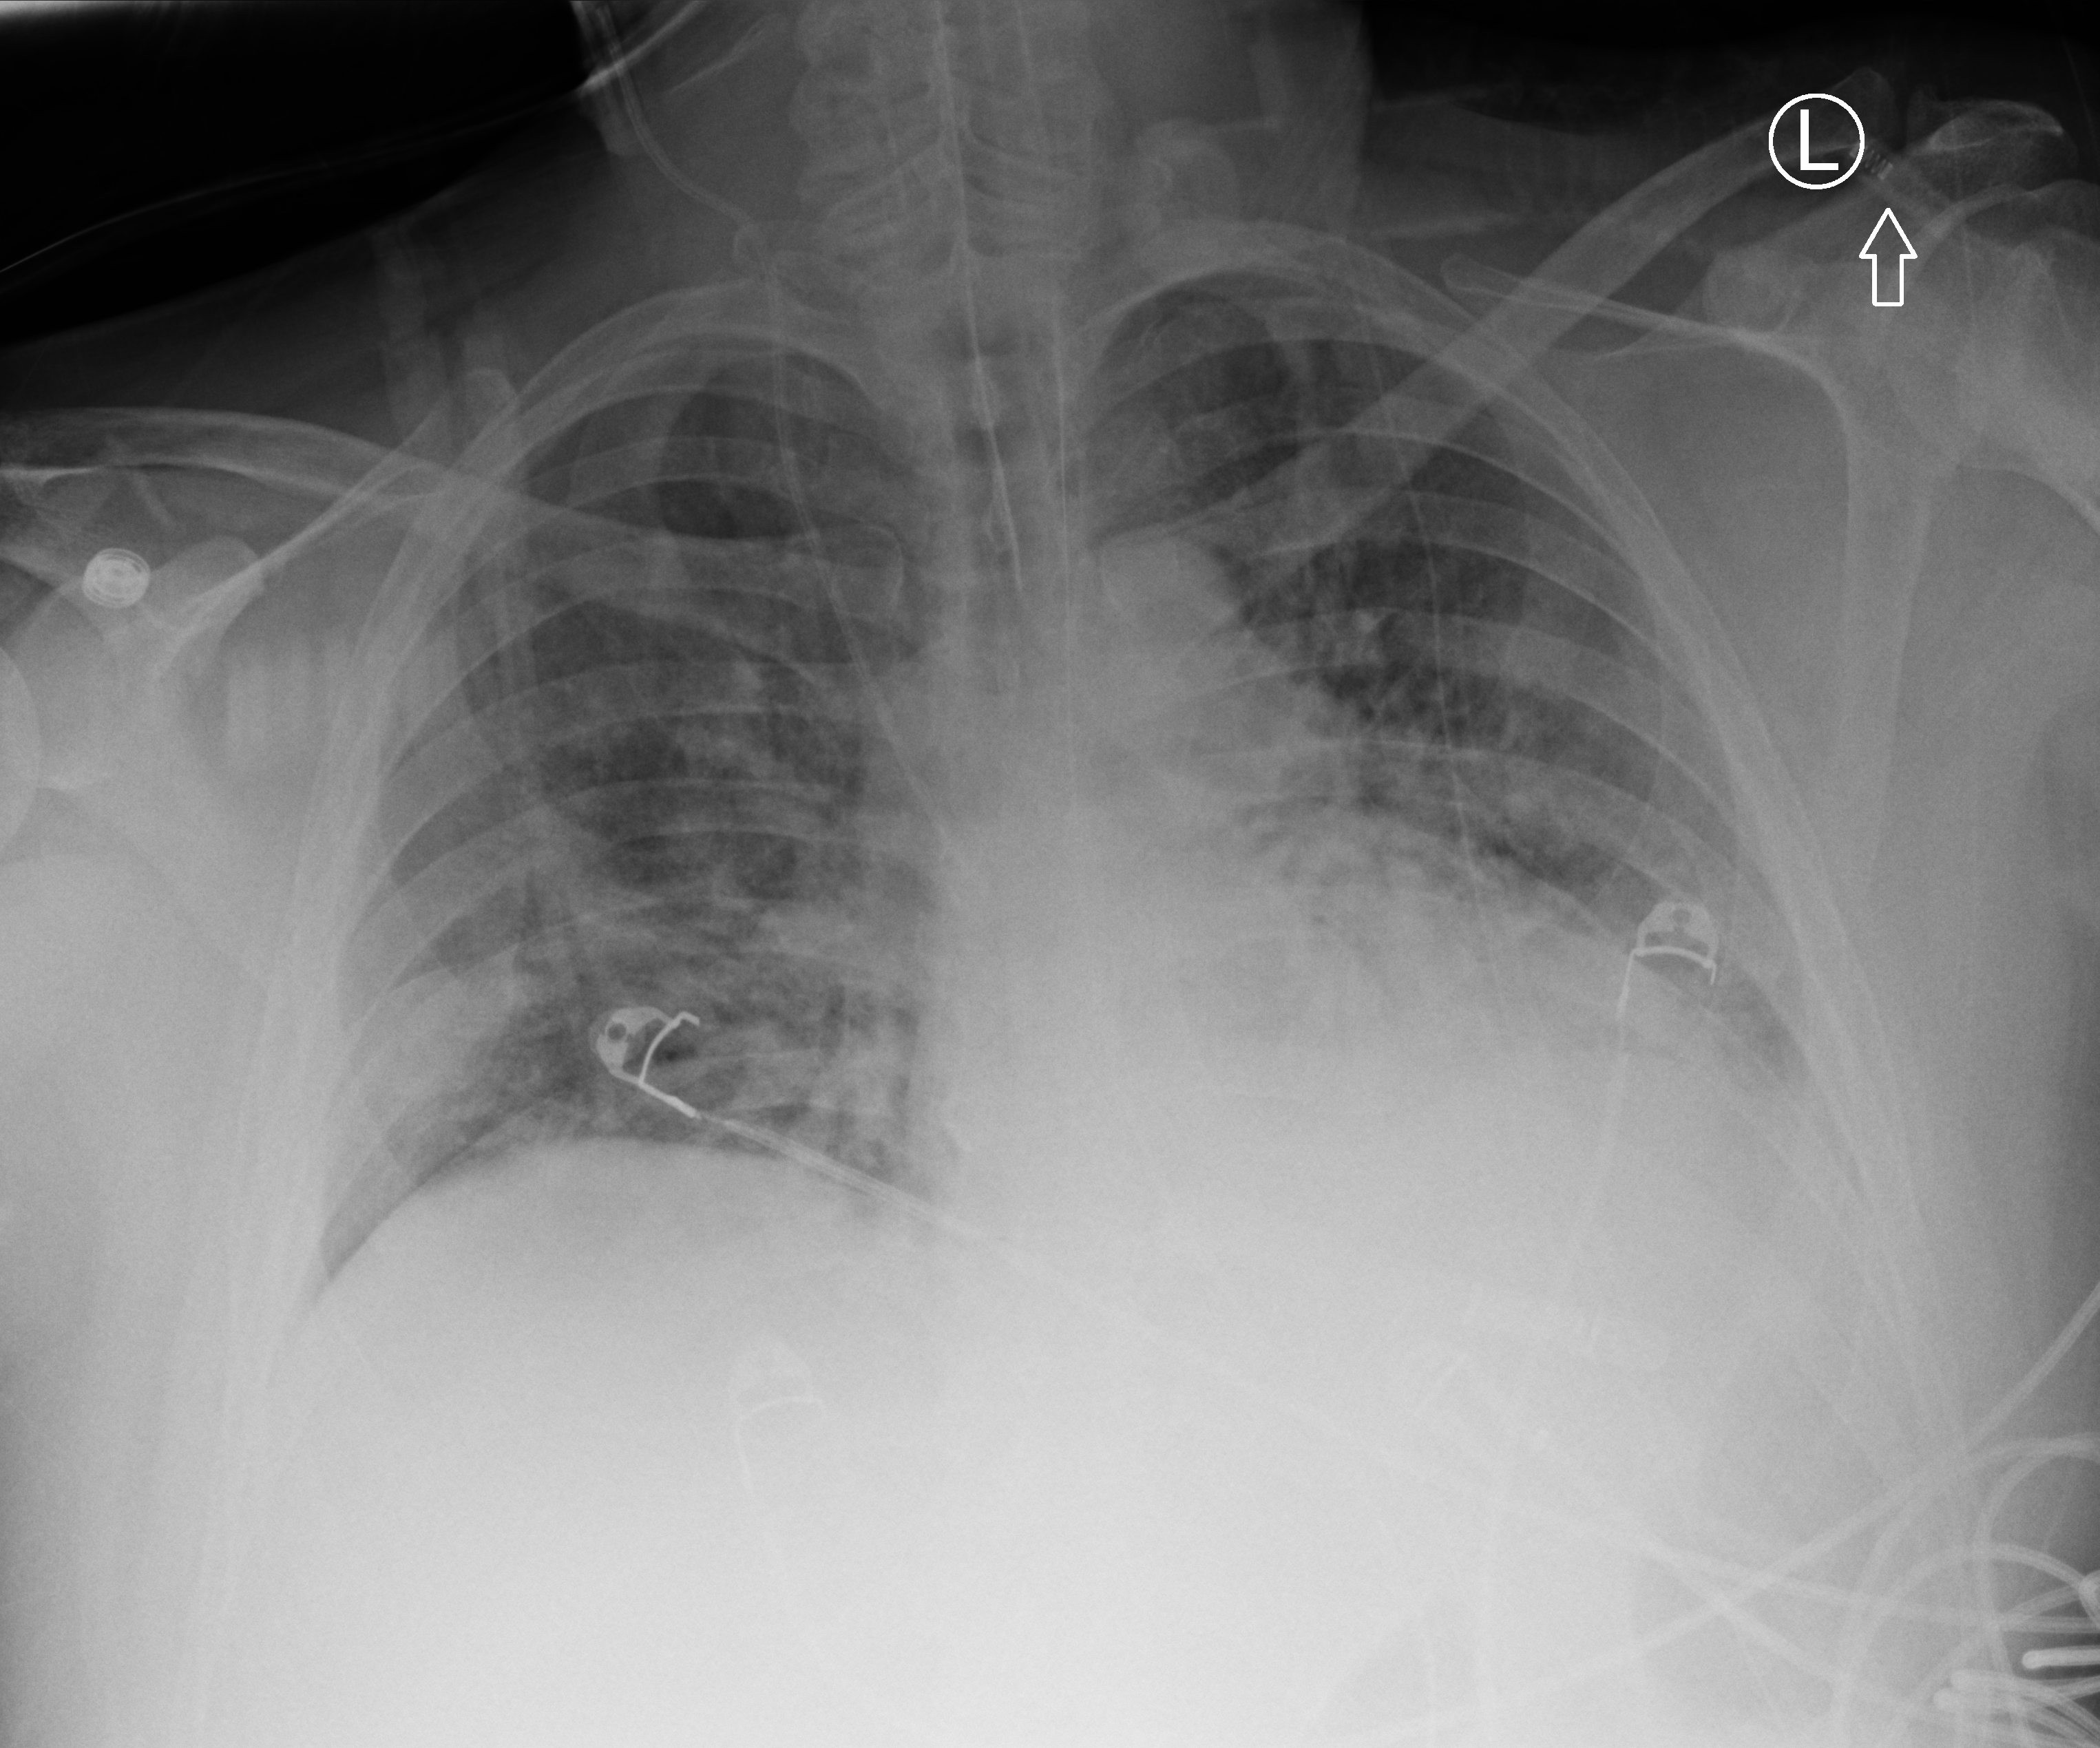
Portable chest radiograph; anteroposterior (AP) projection. Patient hospitalised with COVID-19; male, aged 18–59 years.
From the hospital-stay record, not from the radiograph (when in the stay this image was taken is not recorded):
- admitted to intensive care during this hospital stay: yes
- COPD (admission record): no
- mechanically ventilated during this hospital stay: yes